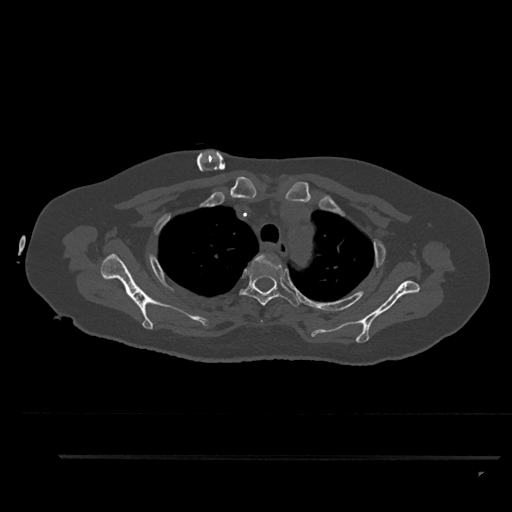
CT including the spine, one axial slice; position 689 of 797 along the scan axis; reconstruction kernel Br40s/3; bone window (W 1800 / L 400 HU); 0.5 mm slice thickness; 512 × 512 image matrix, field of view 408 × 408 mm. Female patient, age 44 years. Case-level facts recorded for this patient, not image findings: primary cancer: renal.
Annotated regions visible in this slice (semi-automatically segmented with operator editing):
- T2 vertebra: bounding box <261,320,263,322> (left, top, right, bottom; pixels)
- T3 vertebra: <239,254,300,307>